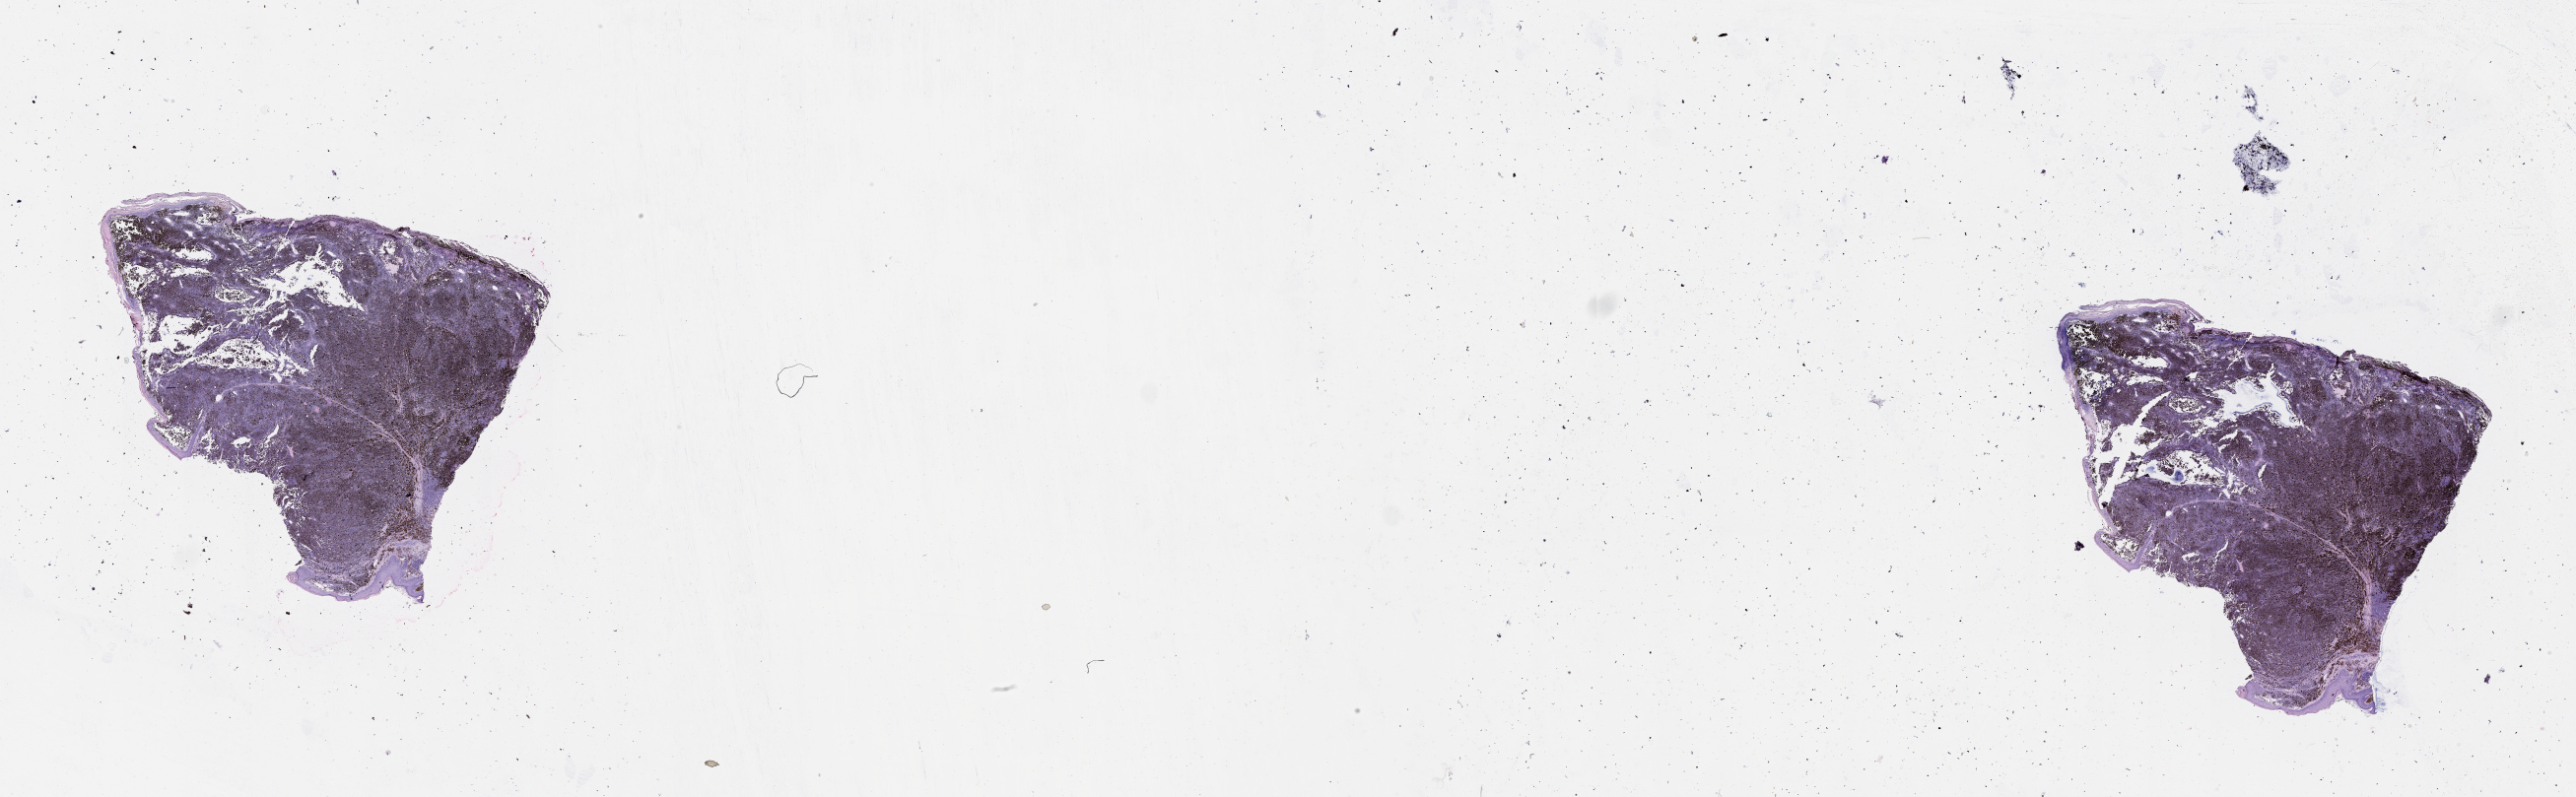
H&E whole-slide image — whole scanned area (about 42.1 x 13.0 mm) shown as a low-resolution overview, melanoma tumour tissue; sampled site not recorded. 83-year-old male patient.
• AJCC pathologic stage: IIC
• diagnosis: Malignant melanoma, NOS
• primary tumour site (as recorded): head & neck